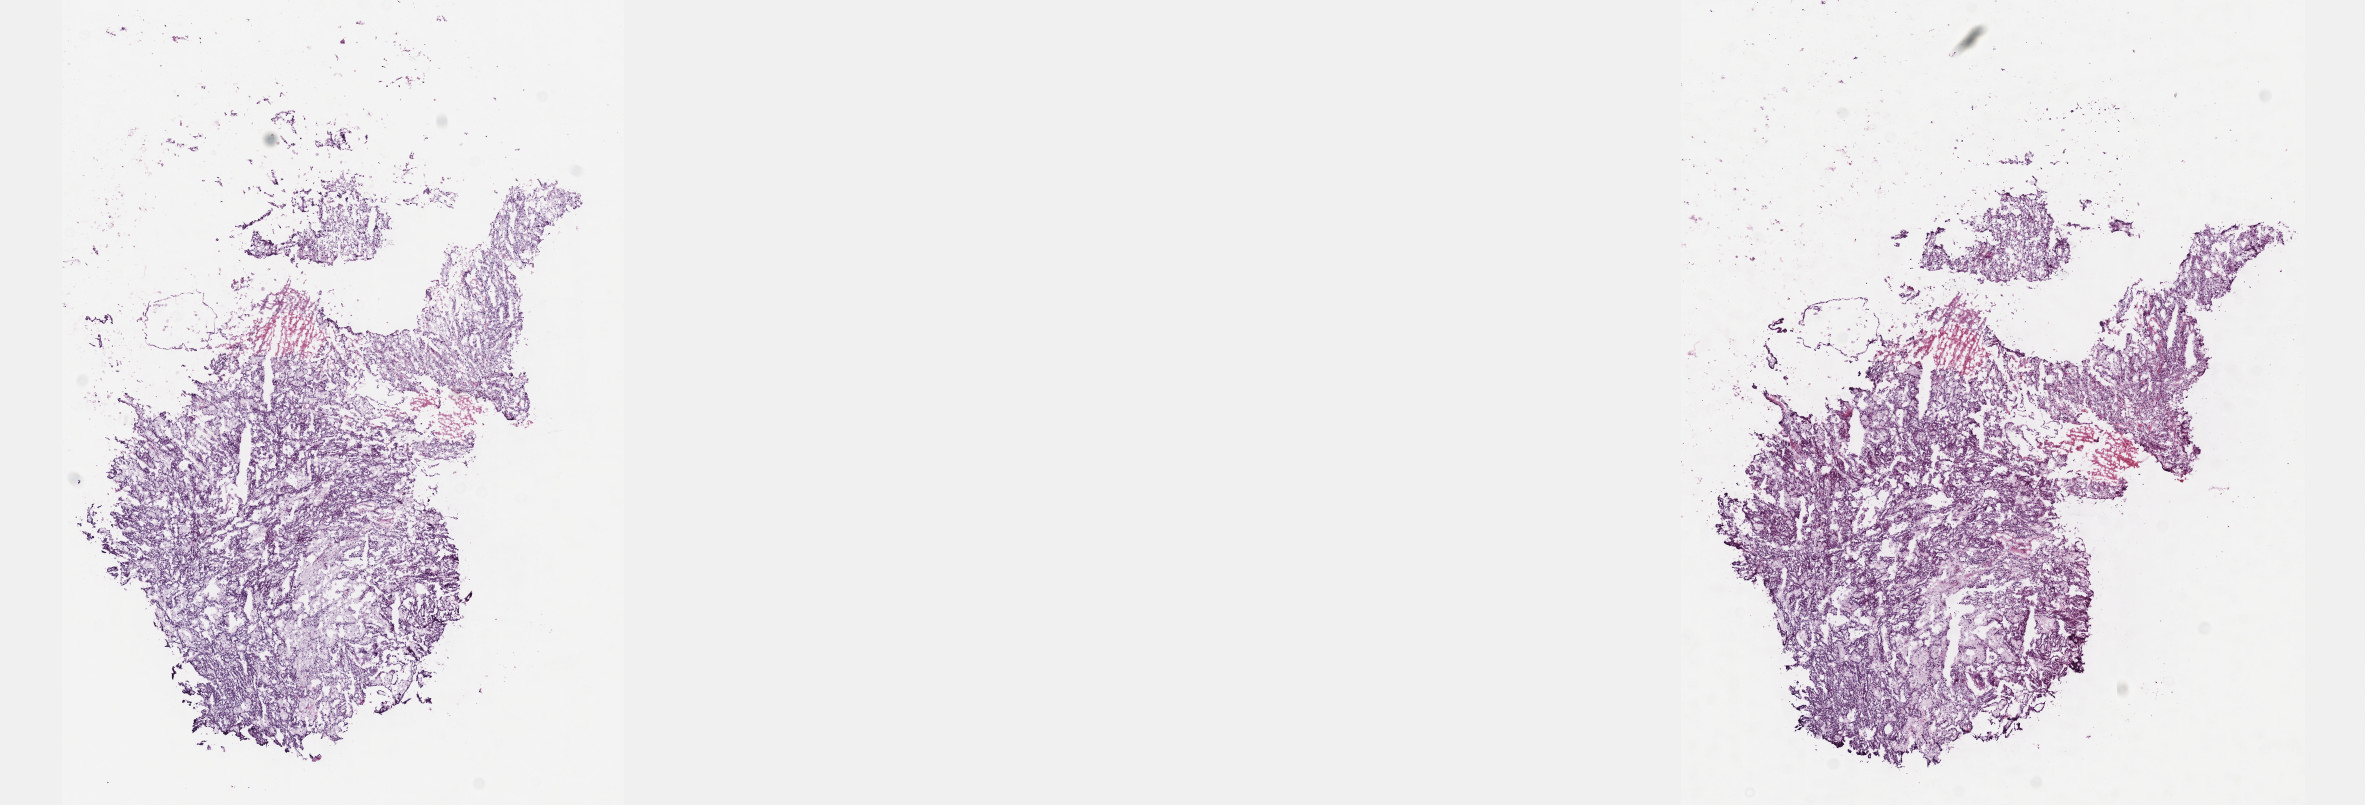
H&E-stained whole-slide image, whole scanned area (about 19.1 x 6.5 mm, slide scanned at 40x) shown as a low-resolution overview, frozen section from the top of the tissue portion, kidney, primary tumour sample. Male, age 66 years at initial diagnosis. Composition of this section per pathologist review: tumour cells 85%, tumour nuclei 90%, normal cells 0%, stromal cells 5%, necrosis 10%. Infiltration values recorded for this section: lymphocyte infiltration 0%, monocyte infiltration 0%, neutrophil infiltration 0%.
Histologic diagnosis: Papillary adenocarcinoma, NOS. AJCC pathologic stage: II (7th edition).